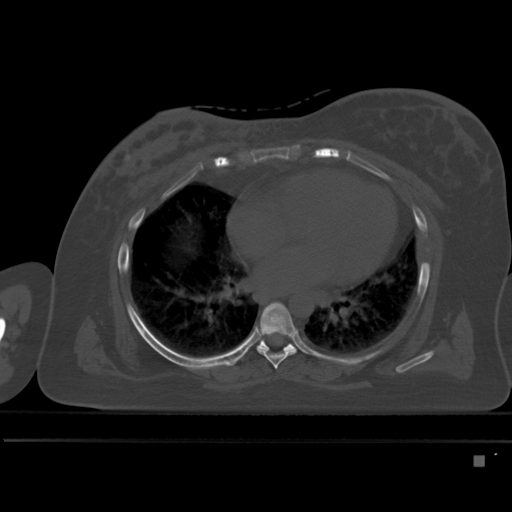
CT including the spine, one axial slice. Position 300 of 495 along the scan axis. Bone window (W 1800 / L 400 HU). 512 × 512 image matrix, field of view 404 × 404 mm. Patient: female, 33 years. Case-level facts recorded for this patient, not image findings: primary cancer: breast; vertebrae with lytic lesions (as recorded): T1.
Annotated regions visible in this slice (semi-automatically segmented with operator editing):
- T6 vertebra: bounding box <258,303,296,370> (left, top, right, bottom; pixels)
- T7 vertebra: <244,339,294,355>